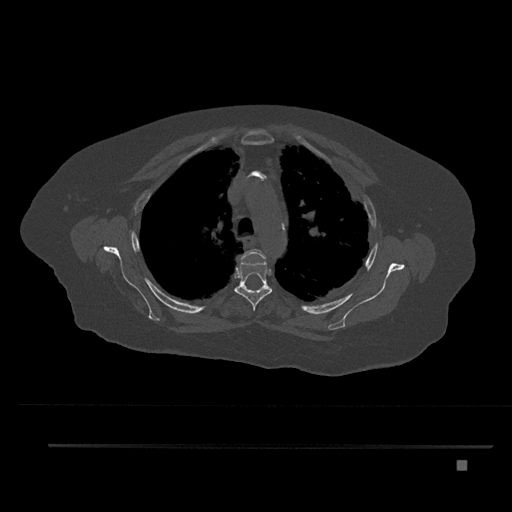
CT including the spine, one axial slice; slice 604 of 797 in the series (ordered by position); reconstruction kernel Br40s/3; bone window (W 1800 / L 400 HU); 0.5 mm slice thickness; 512 × 512 image matrix, field of view 437 × 437 mm. Patient: female, 76 years. Case-level facts recorded for this patient, not image findings: primary cancer: lung.
Outlined on this slice (semi-automatically segmented with operator editing):
- T3 vertebra: bounding box (x1, y1, x2, y2) in pixels: (241, 249, 266, 262)
- T4 vertebra: (234, 256, 273, 311)
- T5 vertebra: (246, 288, 252, 291)